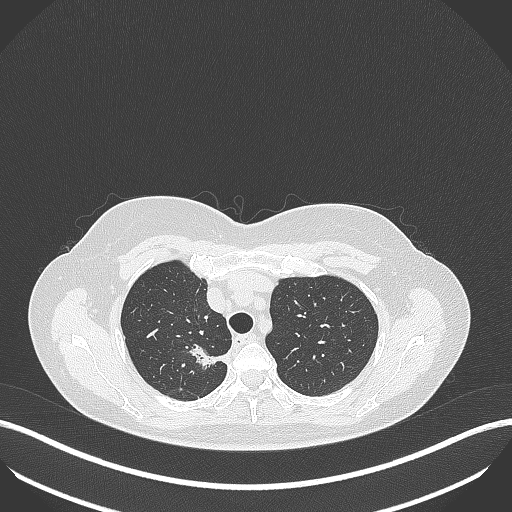
Chest CT, one axial slice. Slice 310 of 386 in the series (ordered by position). Reconstruction kernel B70f. 120 kVp. Lung window (W 1500 / L -600 HU). 512 × 512 image matrix, field of view 400 × 400 mm. Patient: female, 65 years. Case-level facts recorded for this patient, not image findings: clinical TNM (as recorded): T1b N0 M0.
Structures marked on this image (bounding box drawn by a radiologist):
- lung tumour (recorded histology: adenocarcinoma): box from (x=188, y=341) to (x=232, y=375) px